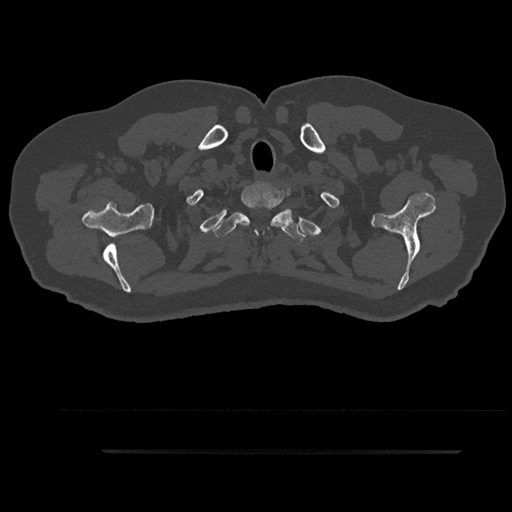
CT including the spine, one axial slice. Slice 780 of 797 in the series (ordered by position). 120 kVp. Bone window (W 1800 / L 400 HU). 512 × 512 image matrix, field of view 432 × 432 mm. Male patient, age 63 years. From the clinical record (not read from this slice): primary cancer: renal; vertebrae with lytic lesions (as recorded): T8.
Annotated regions visible in this slice (semi-automatic segmentation, software-assisted and operator-edited):
- T1 vertebra: bounding box (x1, y1, x2, y2) in pixels: (231, 185, 284, 234)
- T2 vertebra: (213, 206, 306, 241)